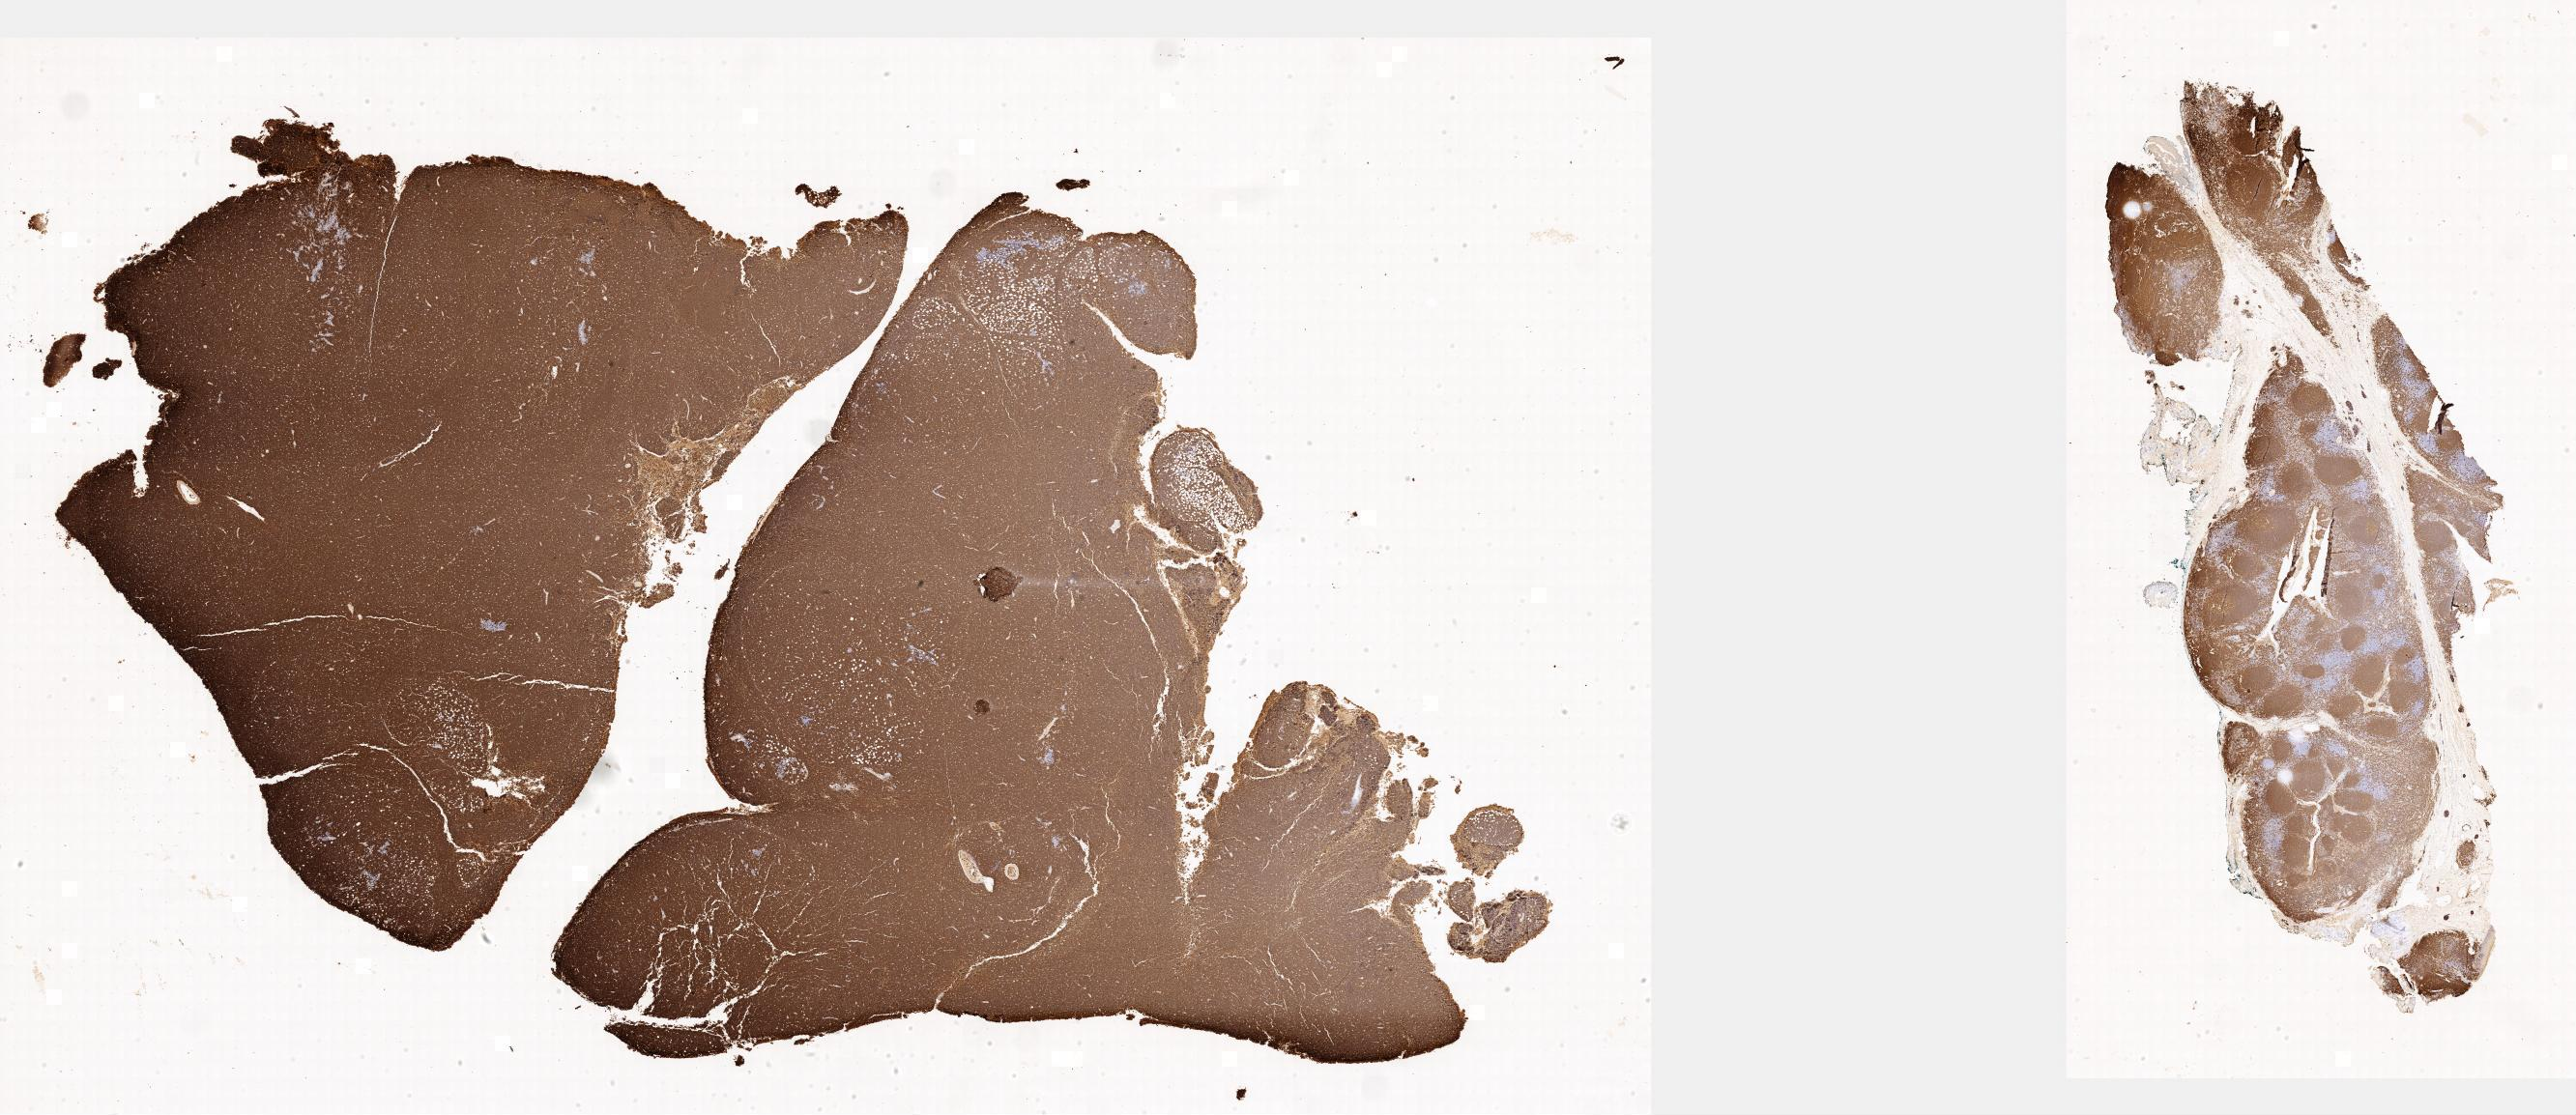
Immunohistochemistry (IHC) whole-slide image stained for CD20 — whole scanned area shown as a low-resolution overview, specimen: tumor tissue, anatomic site: peritoneum. Male, age 9 years at initial diagnosis.
Diagnosis: Burkitt lymphoma, NOS.